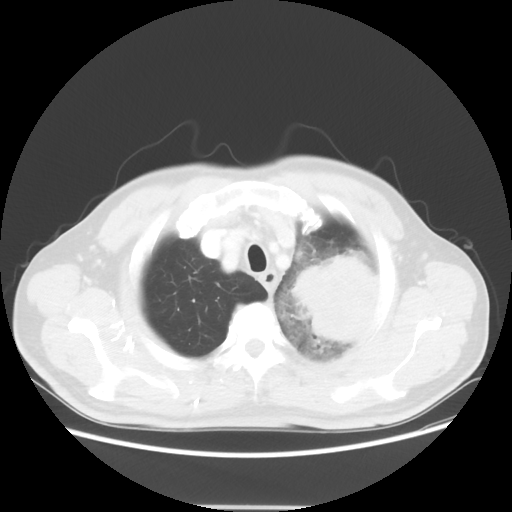
Chest CT, one axial slice; 100 kVp; lung window (W 1500 / L -600 HU); 5 mm slice thickness; 512 × 512 image matrix. Male patient, age 60 years. From the clinical record (not read from this slice): clinical TNM (as recorded): T4 N1 M1a; histopathological grade: G3.
Outlined on this slice (bounding box drawn by a radiologist):
- lung tumour (recorded histology: large cell carcinoma): bounding box [x1, y1, x2, y2] px = [283, 243, 392, 367]